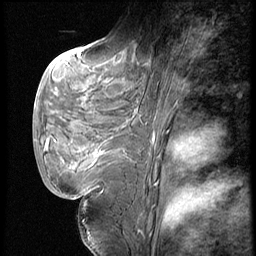
Breast MRI (dynamic contrast-enhanced), one sagittal slice. Position 25 of 62 along the scan axis. Dynamic contrast-enhanced series, image 2 of 4 at this slice position (ordered by acquisition). 1.5 T. TE 4.2 ms, TR 9 ms. 256 × 256 image matrix, field of view 180 × 180 mm. Patient: female, 28 years. From the clinical record (not read from this slice): setting: breast cancer imaged before/during neoadjuvant chemotherapy.
Outlined on this slice (semi-automatic segmentation, software-assisted and operator-edited):
- analysis volume of interest (the breast-tissue region the enhancement analysis was run in; not a lesion): bounding box (x1, y1, x2, y2) in pixels: (40, 54, 150, 183)
- tumour enhancement mask (voxels above the 140 % enhancement threshold inside the analysis volume of interest): (86, 145, 101, 157)